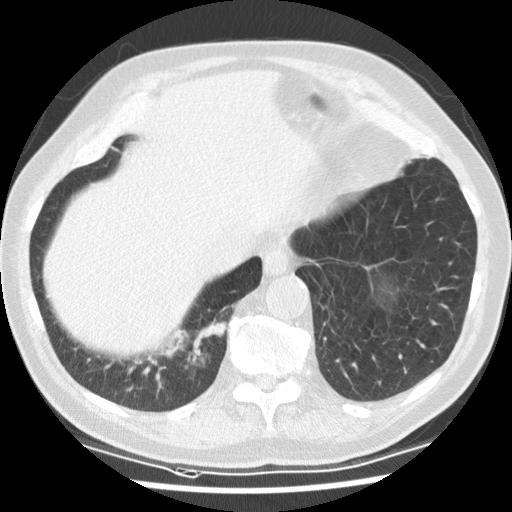
Low-dose screening chest CT, one axial slice; slice 21 of 135 in the series (ordered by position); reconstruction kernel STANDARD; lung window (W 1500 / L -600 HU); 2.5 mm slice thickness; 512 × 512 image matrix, field of view 340 × 340 mm.
Outlined on this slice (expert manual segmentation):
- lesion 2 (nodule, upper lobe of right lung): bounding box [x1, y1, x2, y2] px = [161, 319, 227, 365]